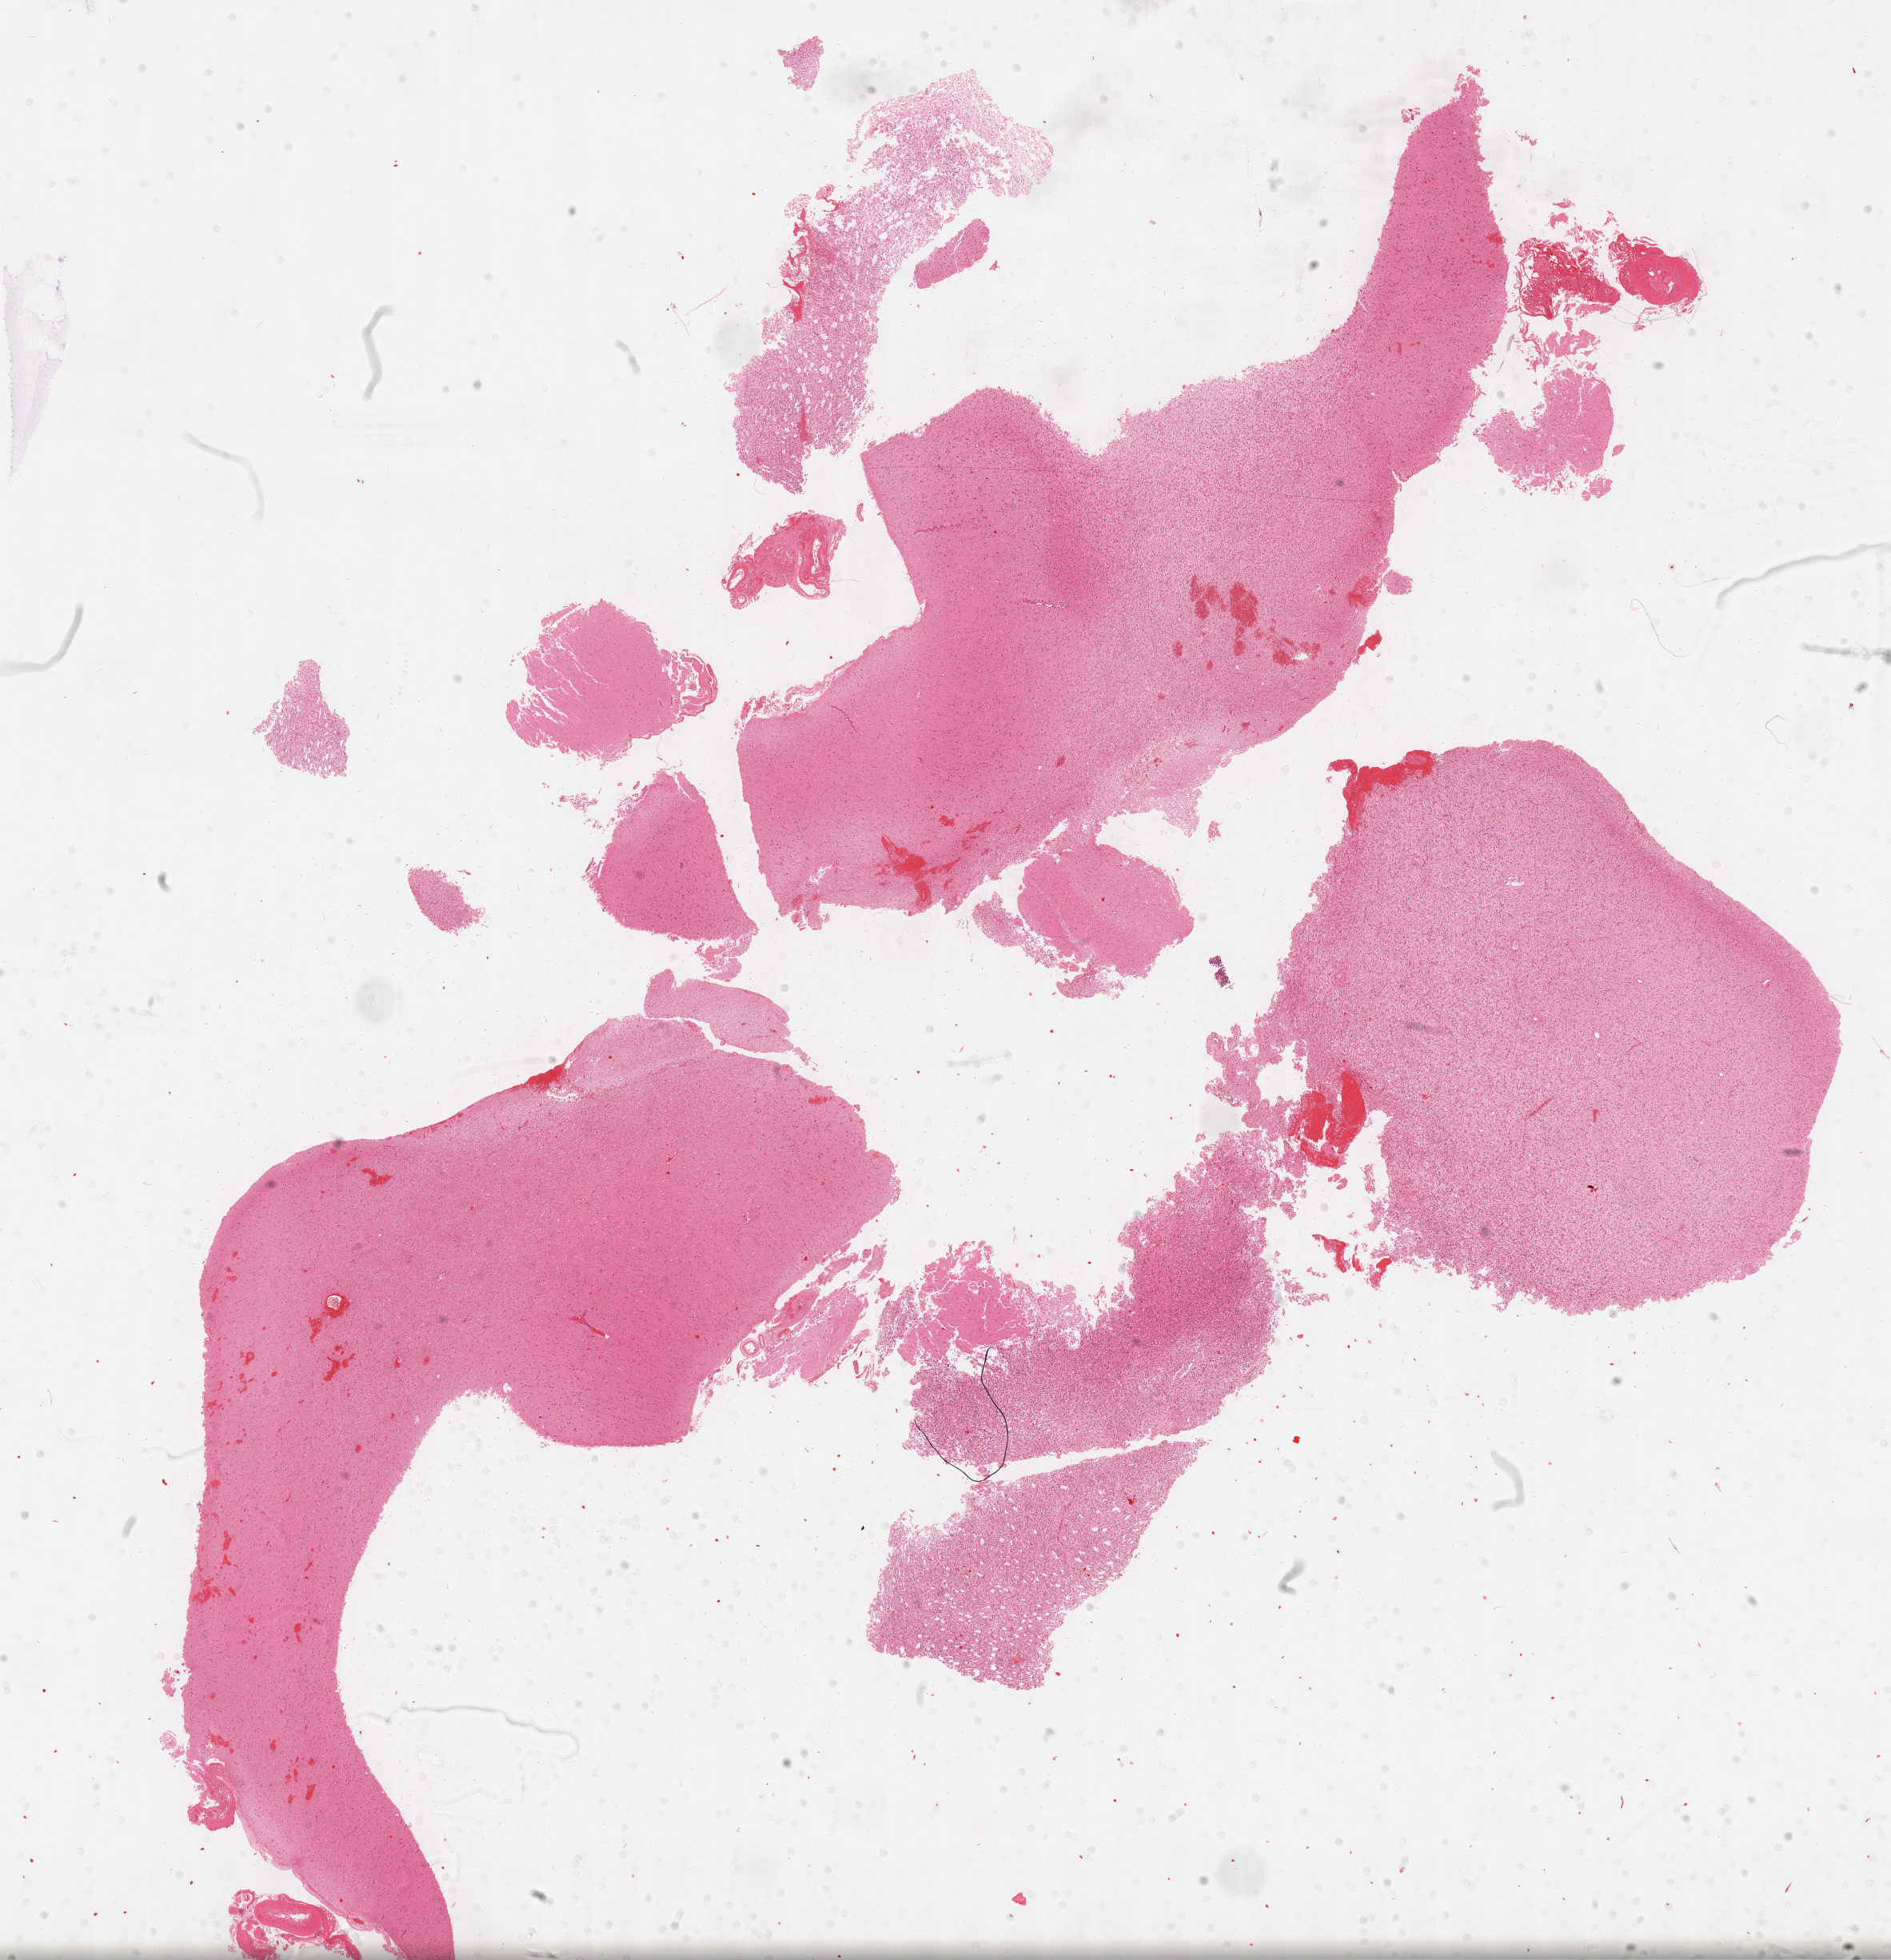
Hematoxylin and eosin (H&E) stained whole-slide image — whole scanned area (about 19.1 x 19.8 mm, slide scanned at 40x) shown as a low-resolution overview, FFPE section, sample: primary tumour, brain. Female patient; age at initial diagnosis 57 years. Histologic grade: G2 (moderately differentiated).
• pathologic diagnosis: Mixed glioma (cerebrum)